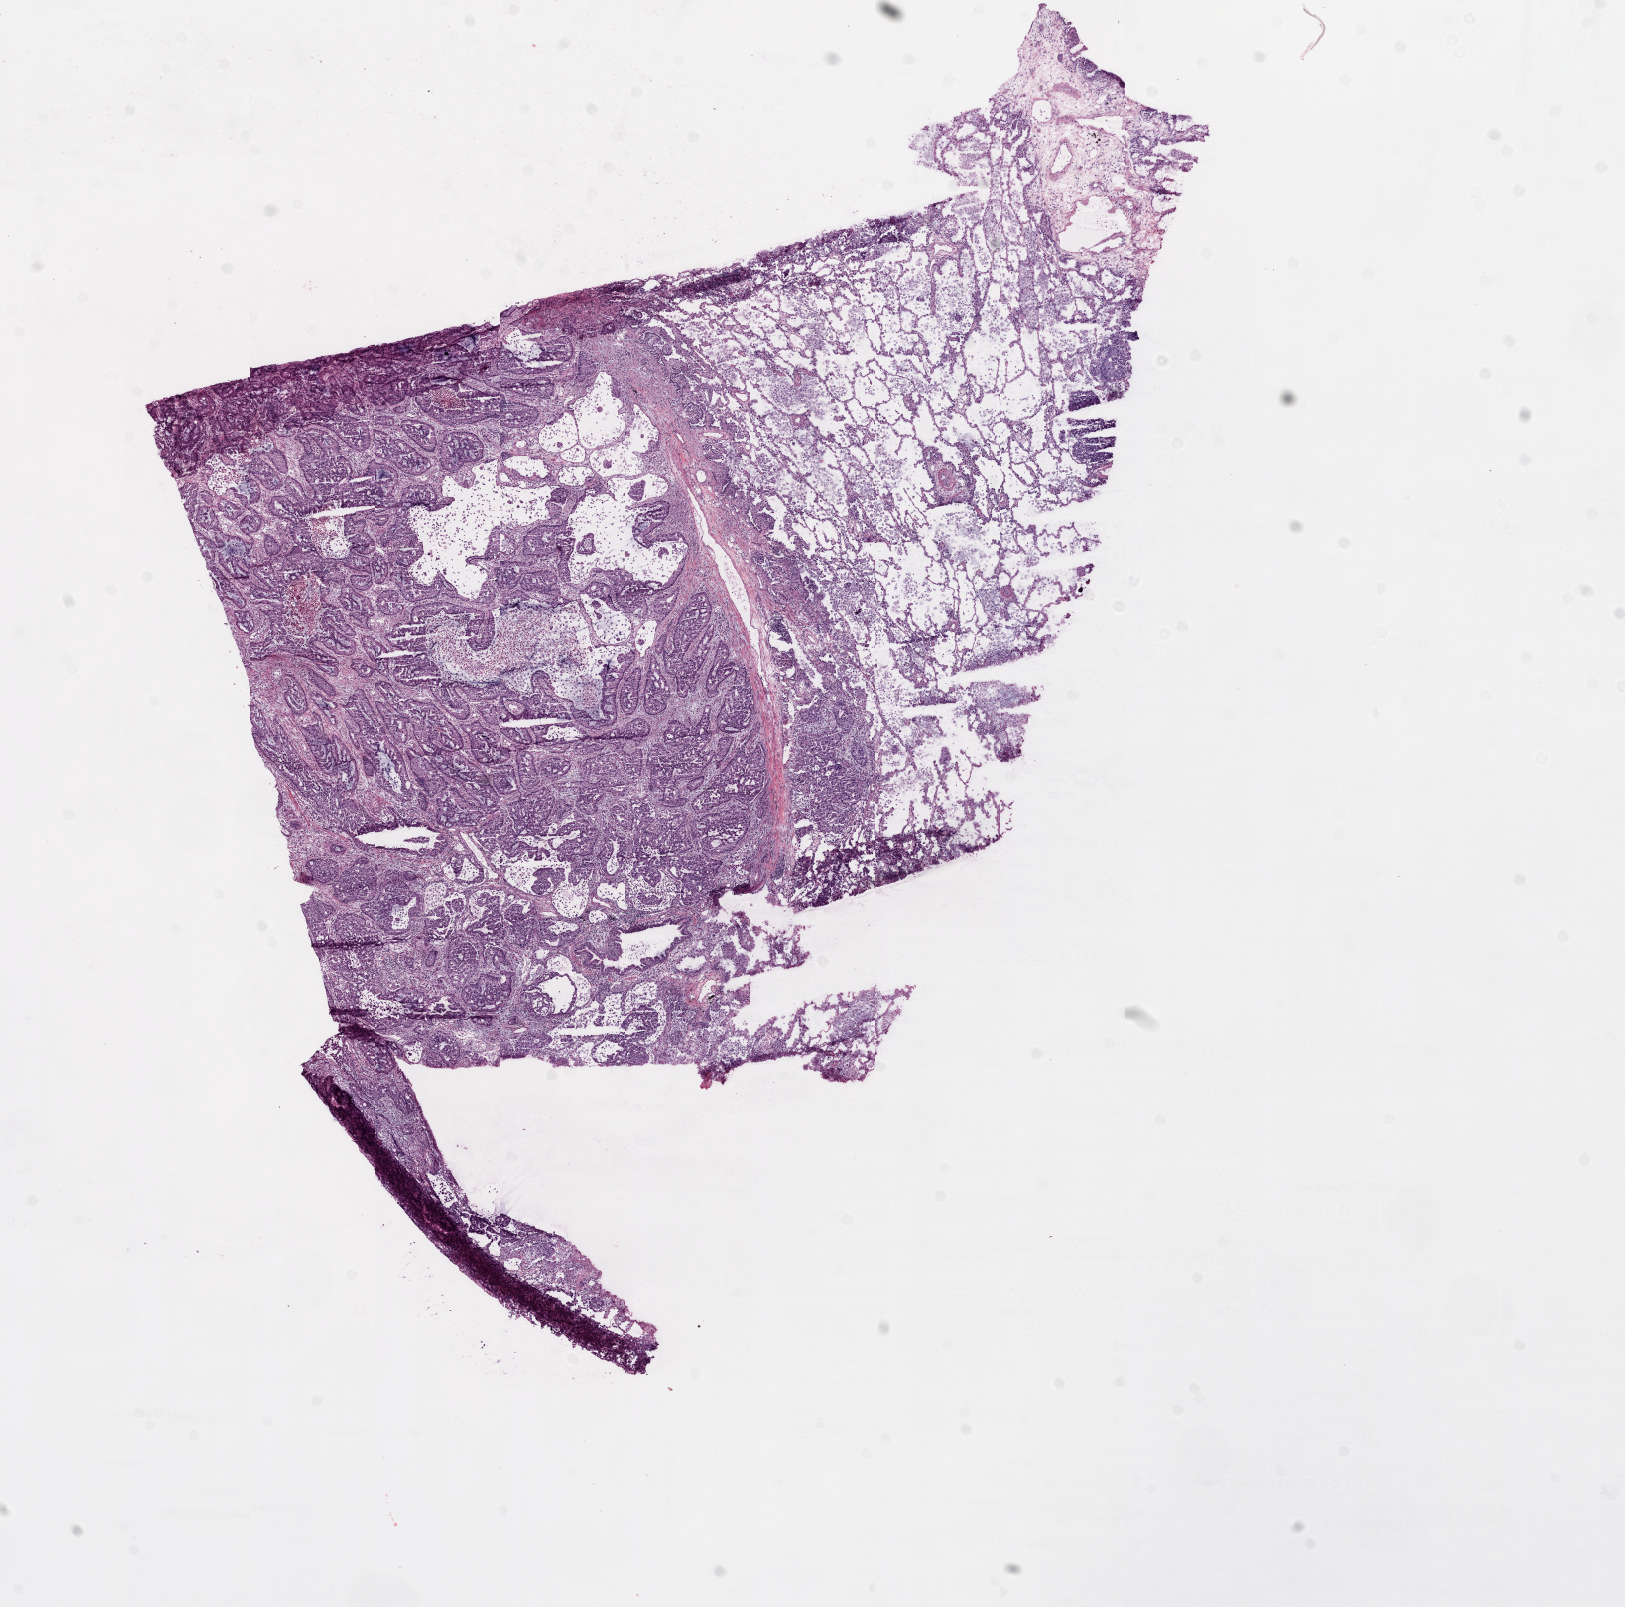
Whole-slide histology image, H&E-stained, shown as a low-resolution overview of the whole scanned area (about 13.0 x 12.9 mm, from a 20x scan), frozen section, lung, primary tumour sample. Male, age 66 years at initial diagnosis. Pathologist review of this section (percent, as recorded): tumour cells 60%, tumour nuclei 80%.
Histologic diagnosis: Adenocarcinoma, NOS.